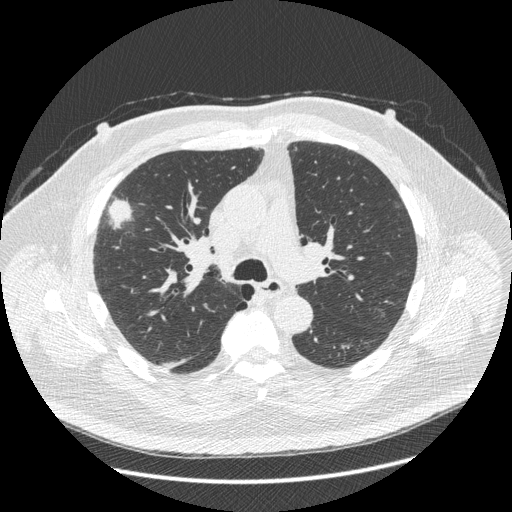
Axial slice from a low-dose chest CT screening exam, third annual screen, lung window (W 1500 / L -600 HU), 1.25 mm slice thickness, 120 kVp, slice 152 of 426 in the series. Male participant, aged 66 years at enrolment. Current smoker at enrolment.
Lesion marked by an expert reader, box from (x=86, y=180) to (x=145, y=264) px. Screening reader's record for this exam (one nodule recorded; not confirmed to be the boxed lesion): non-calcified nodule or mass ≥4 mm, right upper lobe, 48 × 25 mm, spiculated (stellate) margins, soft tissue attenuation, pre-existing on the prior screen: no. Official screen result: positive, other. Lung cancer was diagnosed 35 days after this screen: non-small cell carcinoma, right upper lobe, stage IV (AJCC 6th edition), 50 mm at pathology.